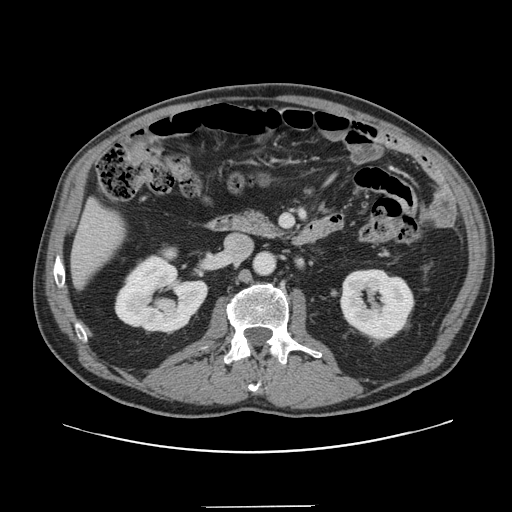
Contrast-enhanced abdominal CT, one axial slice; position 56 of 139 along the scan axis; 120 kVp; soft-tissue window (W 400 / L 40 HU); 2.5 mm slice thickness; 512 × 512 image matrix. Male patient, age 64 years. Case-level facts recorded for this patient, not image findings: diagnosis: colorectal cancer liver metastases, imaged before liver resection; multiple liver metastases: yes; largest metastasis: 3.5 cm; disease in both lobes: yes.
Outlined on this slice (outlined manually by an expert reader):
- liver: bounding box (x1, y1, x2, y2) in pixels: (73, 204, 123, 284)
- planned liver remnant (the part of the liver to remain after resection): (72, 204, 124, 284)